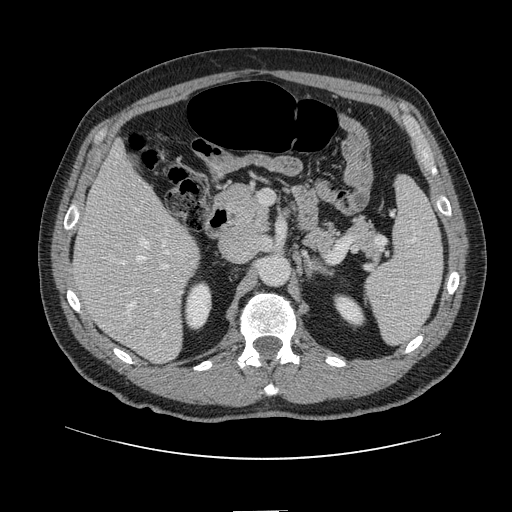
Contrast-enhanced abdominal CT, one axial slice; position 64 of 161 along the scan axis; 120 kVp; soft-tissue window (W 400 / L 40 HU); 2.5 mm slice thickness; 512 × 512 image matrix, field of view 412 × 412 mm. Male patient, age 66 years. From the clinical record (not read from this slice): diagnosis: colorectal cancer liver metastases, imaged before liver resection; multiple liver metastases: no; largest metastasis: 3.5 cm; disease in both lobes: no.
Outlined on this slice (expert manual segmentation):
- hepatic veins: bounding box <122,239,169,336> (left, top, right, bottom; pixels)
- liver: <74,145,200,363>
- planned liver remnant (the part of the liver to remain after resection): <74,145,176,286>
- portal vein (with intrahepatic branches): <119,245,169,314>